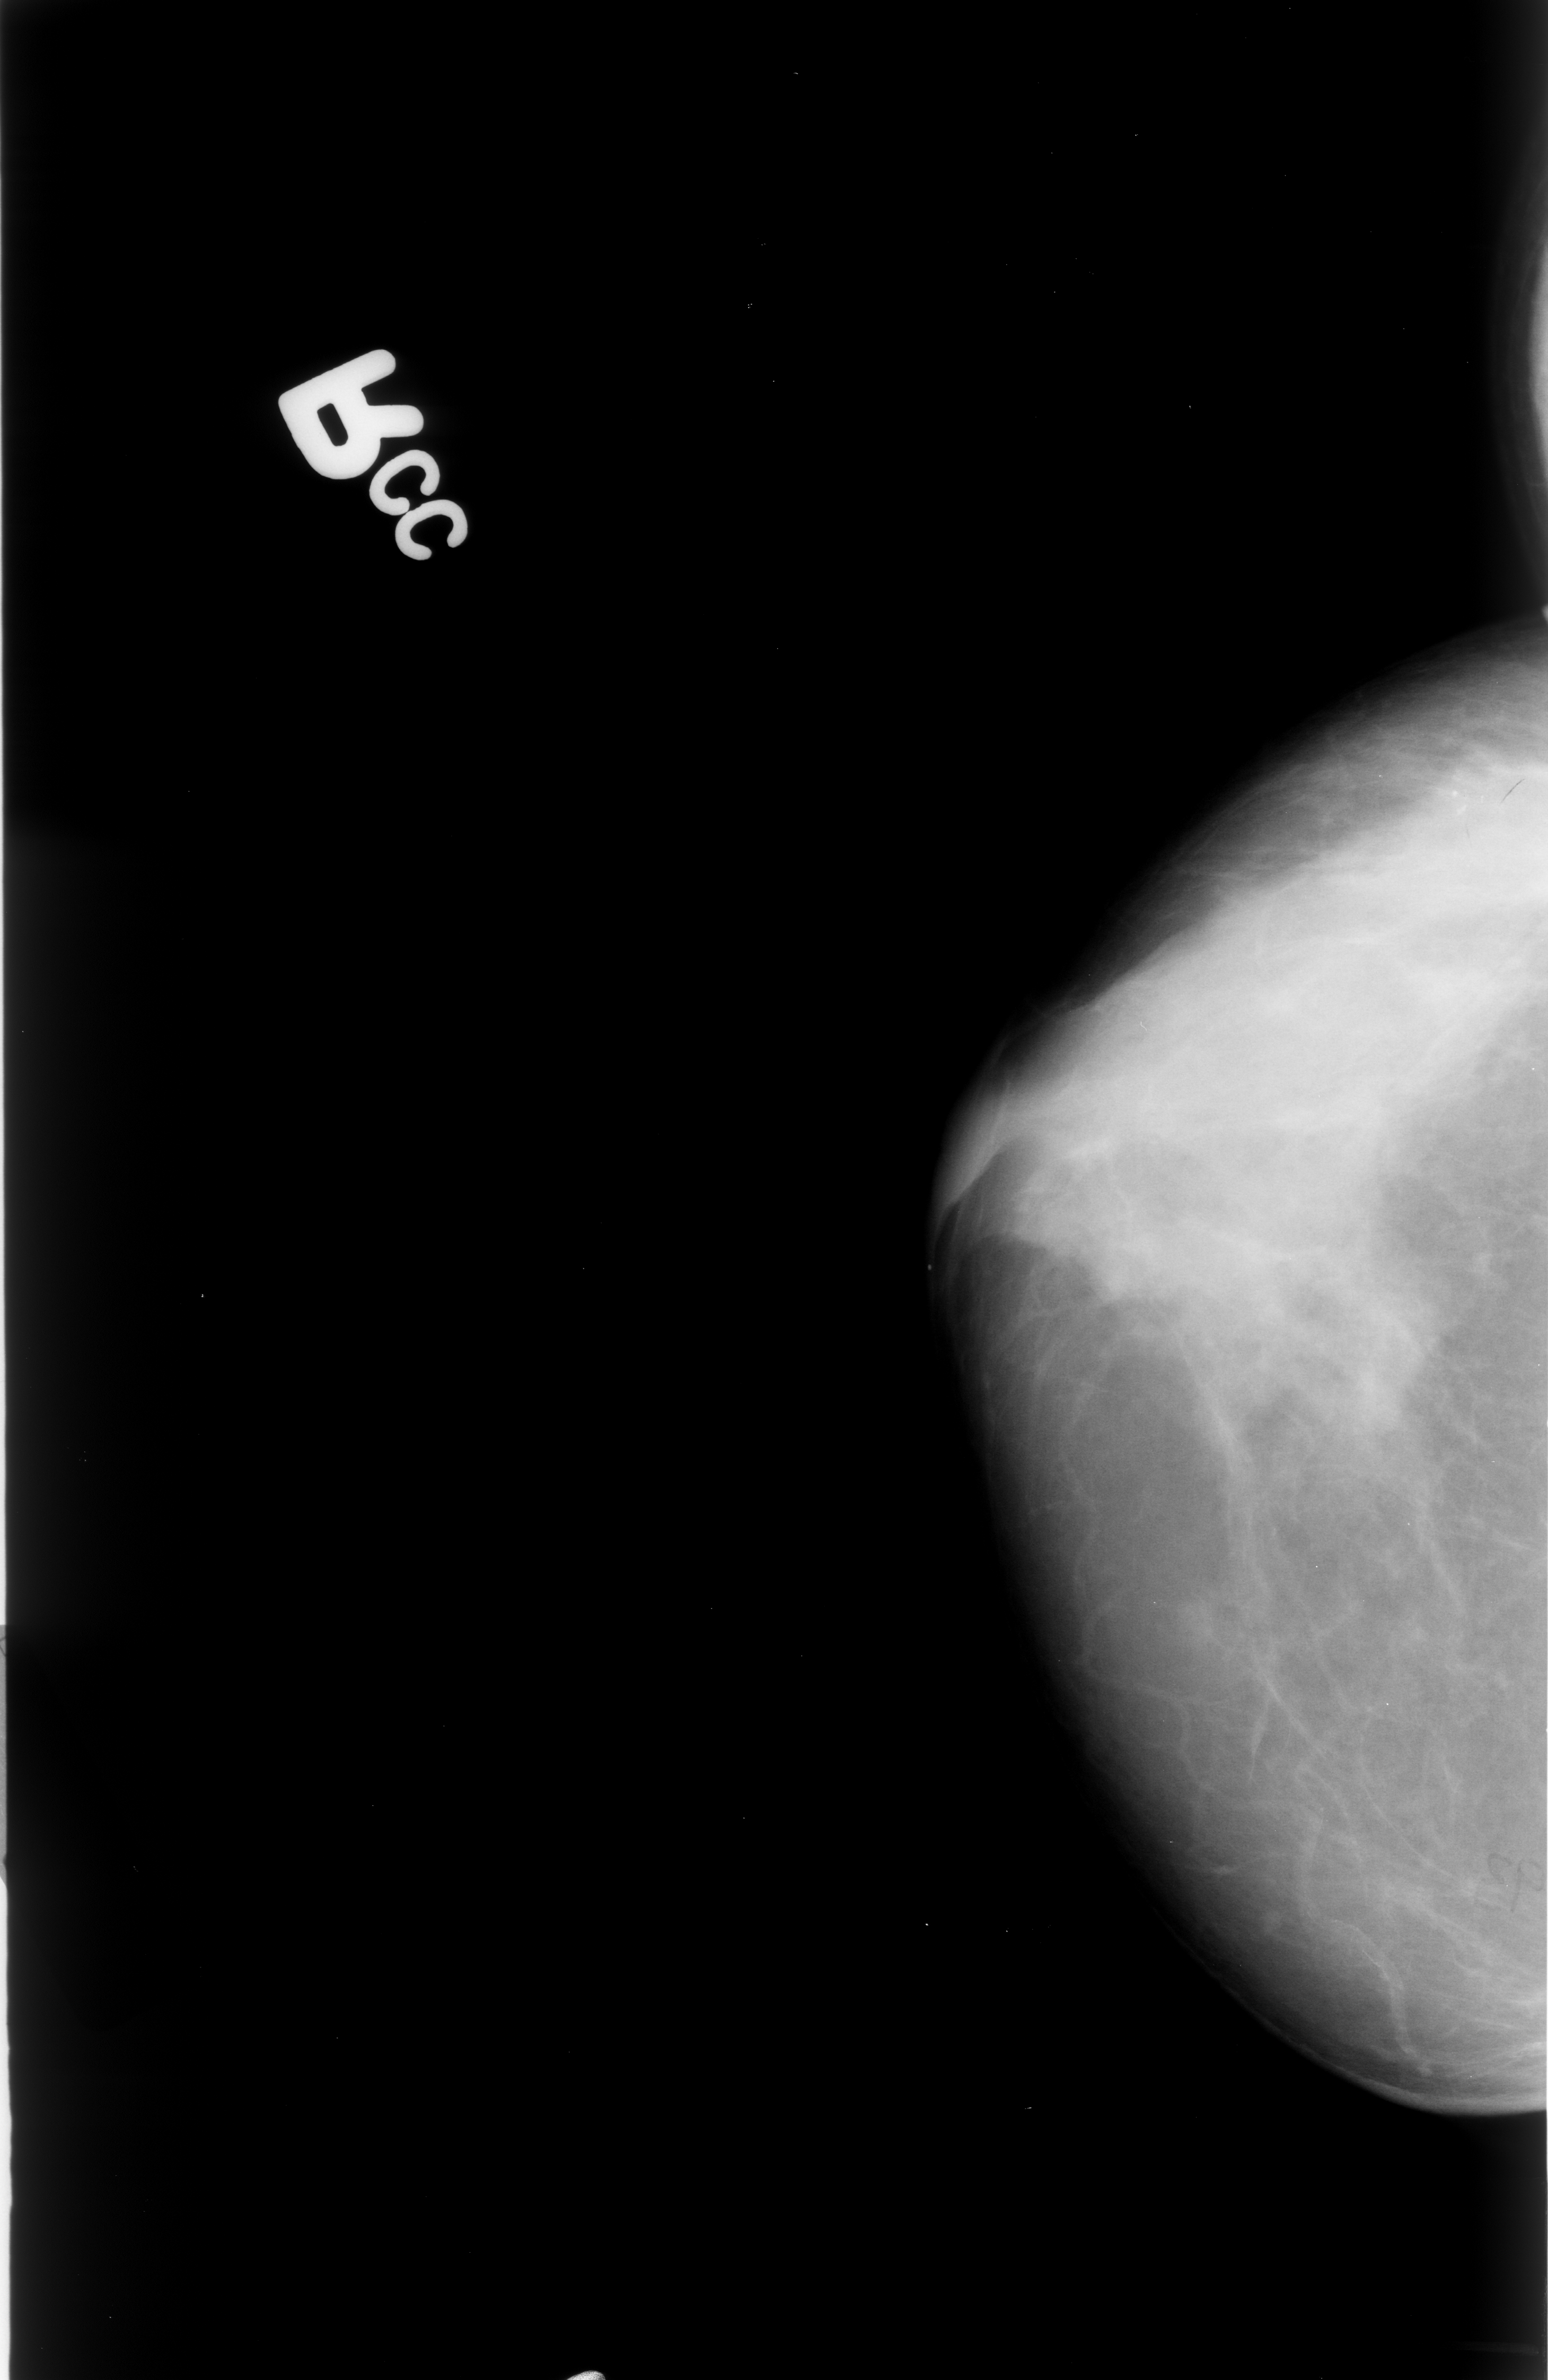
Digitized screen-film mammogram; right breast; CC view; breast composition: heterogeneously dense (BI-RADS density category 3 of 4).
- Marked abnormality: calcifications, morphology pleomorphic, distribution clustered; BI-RADS assessment category 4; pathology result (as recorded, not read from the image): malignant.